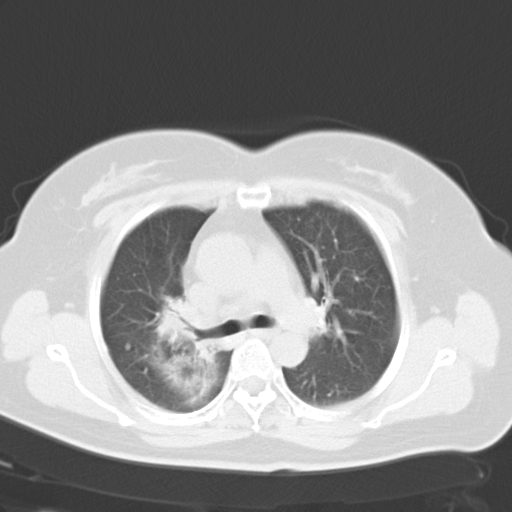
Chest CT, one axial slice; position 21 of 30 along the scan axis; lung window (W 1500 / L -600 HU); 8 mm slice thickness; 512 × 512 image matrix, field of view 353 × 353 mm. Patient: female, 50 years. From the clinical record (not read from this slice): clinical TNM (as recorded): T2a N0 M1a.
Outlined on this slice (rectangle marked by the reading radiologist):
- lung tumour (recorded histology: adenocarcinoma): bounding box [x1, y1, x2, y2] px = [151, 289, 222, 370]